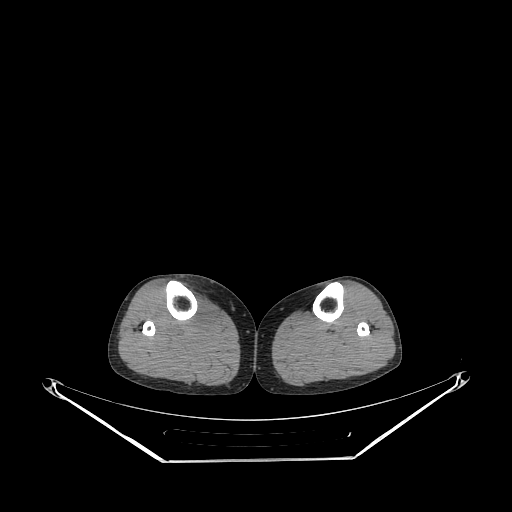
CT of an extremity soft-tissue mass (from a PET/CT study), one axial slice; slice 147 of 267 in the series (ordered by position); reconstruction kernel STANDARD; 140 kVp; soft-tissue window (W 400 / L 40 HU); 3.75 mm slice thickness; 512 × 512 image matrix, field of view 500 × 500 mm. Female patient. From the clinical record (not read from this slice): histological type: undifferentiated – high grade; grade: high; site of the primary tumour: right thigh.
Annotated regions visible in this slice (expert contour drawn on MRI and transferred to this co-registered scan by the dataset authors):
- gross tumour volume (mass): bounding box <185,295,216,332> (left, top, right, bottom; pixels)